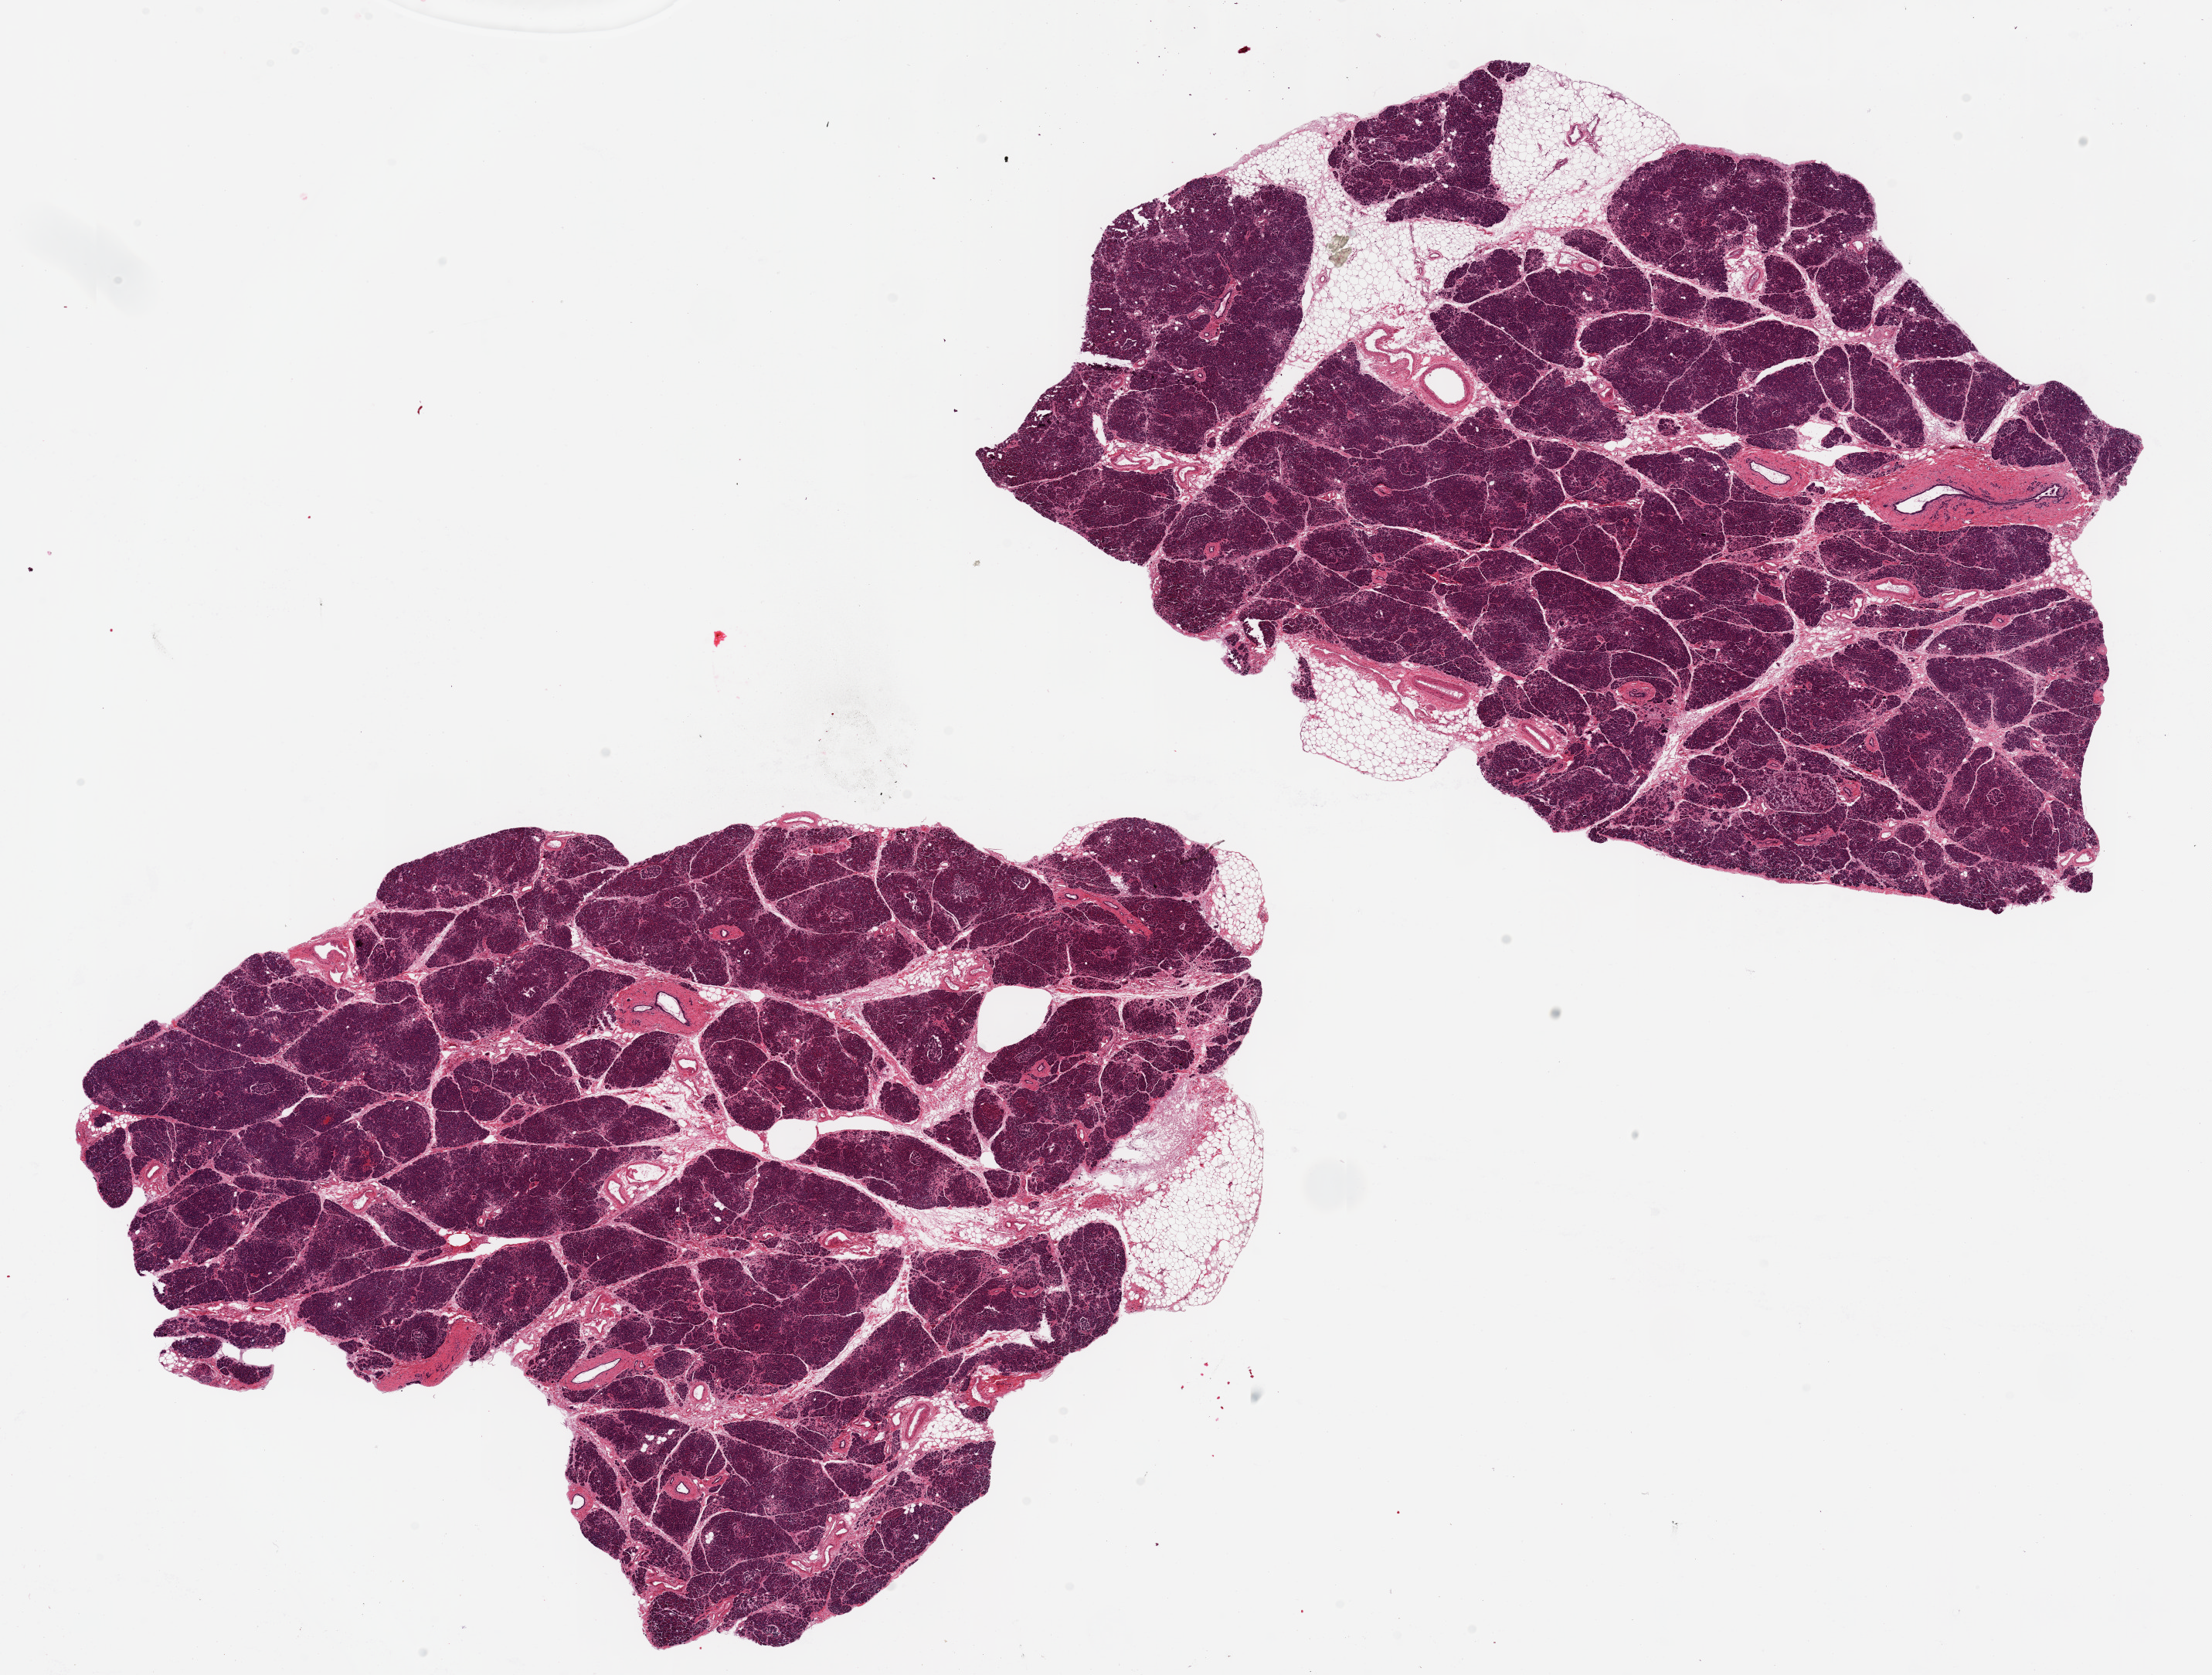
Digitized hematoxylin and eosin (H&E)-stained section, shown as a low-resolution overview of the whole scanned area (about 22.6 x 17.1 mm). PAXgene-fixed paraffin-embedded (PFPE) section. Target tissue: pancreas. Donor tissue sample. Donor sex: male.
Pathologist's review note for this sample: 2 pieces 11.9x8 & 9x9 mm; well formed islets ~230um; focal interstitial fibrosis; ~10% interstitial fat.